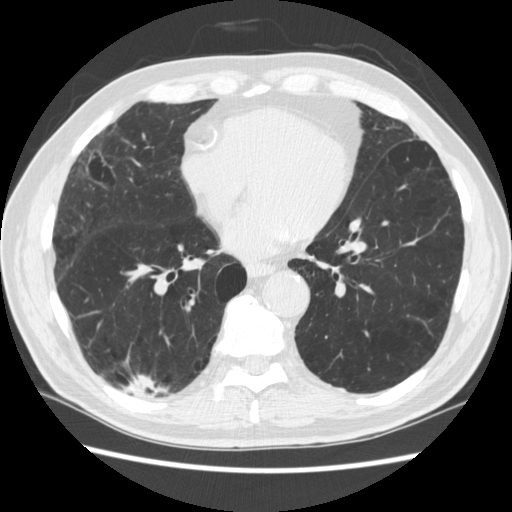
Low-dose screening chest CT, axial slice, third annual screen, lung window (W 1500 / L -600 HU), 1.25 mm slice thickness, standard (soft-tissue) reconstruction kernel (STANDARD), slice 156 of 266 in the series. Male participant, aged 70 years at enrolment. Former smoker at enrolment.
• Lesion marked by an expert reader, bounding box (x1, y1, x2, y2) in pixels: (127, 360, 179, 416).
• The screening reader recorded 4 non-calcified nodules or masses ≥4 mm on this exam (right lower lobe, right lower lobe, left lower lobe, left lower lobe); which of them this box marks is not recorded.
• Lung cancer was diagnosed 253 days after this screen: squamous cell carcinoma, NOS, right upper lobe, poorly differentiated (G3), stage IV (AJCC 6th edition).